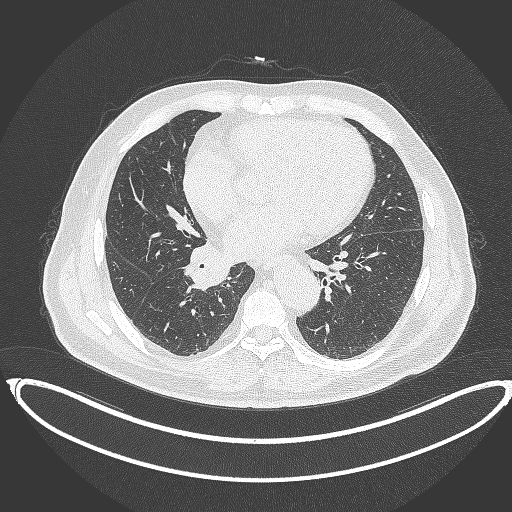
Chest CT, one axial slice; position 179 of 387 along the scan axis; reconstruction kernel B70f; lung window (W 1500 / L -600 HU); 1 mm slice thickness; 512 × 512 image matrix. Patient: male, 61 years. From the clinical record (not read from this slice): clinical TNM (as recorded): T1b N1 M0.
Structures marked on this image (bounding box drawn by a radiologist):
- lung tumour (recorded histology: squamous cell carcinoma): bounding box [x1, y1, x2, y2] px = [180, 238, 231, 291]